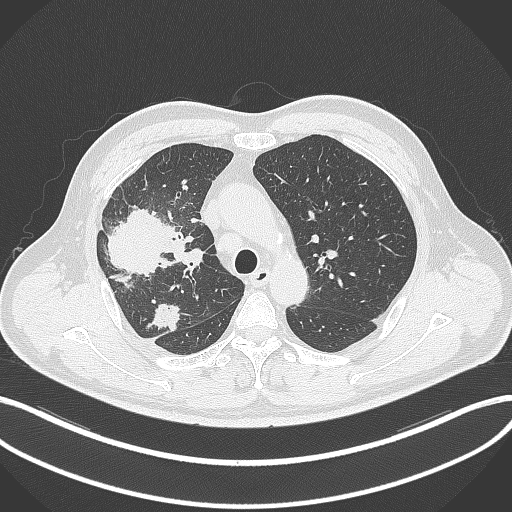
Chest CT, one axial slice. Slice 235 of 348 in the series (ordered by position). 120 kVp. Lung window (W 1500 / L -600 HU). 1 mm slice thickness. 512 × 512 image matrix, field of view 400 × 400 mm. Male patient, age 55 years. From the clinical record (not read from this slice): clinical TNM (as recorded): T3 N2 M1.
Structures marked on this image (bounding box drawn by a radiologist):
- lung tumour (recorded histology: adenocarcinoma): bounding box (x1, y1, x2, y2) in pixels: (101, 203, 177, 289)